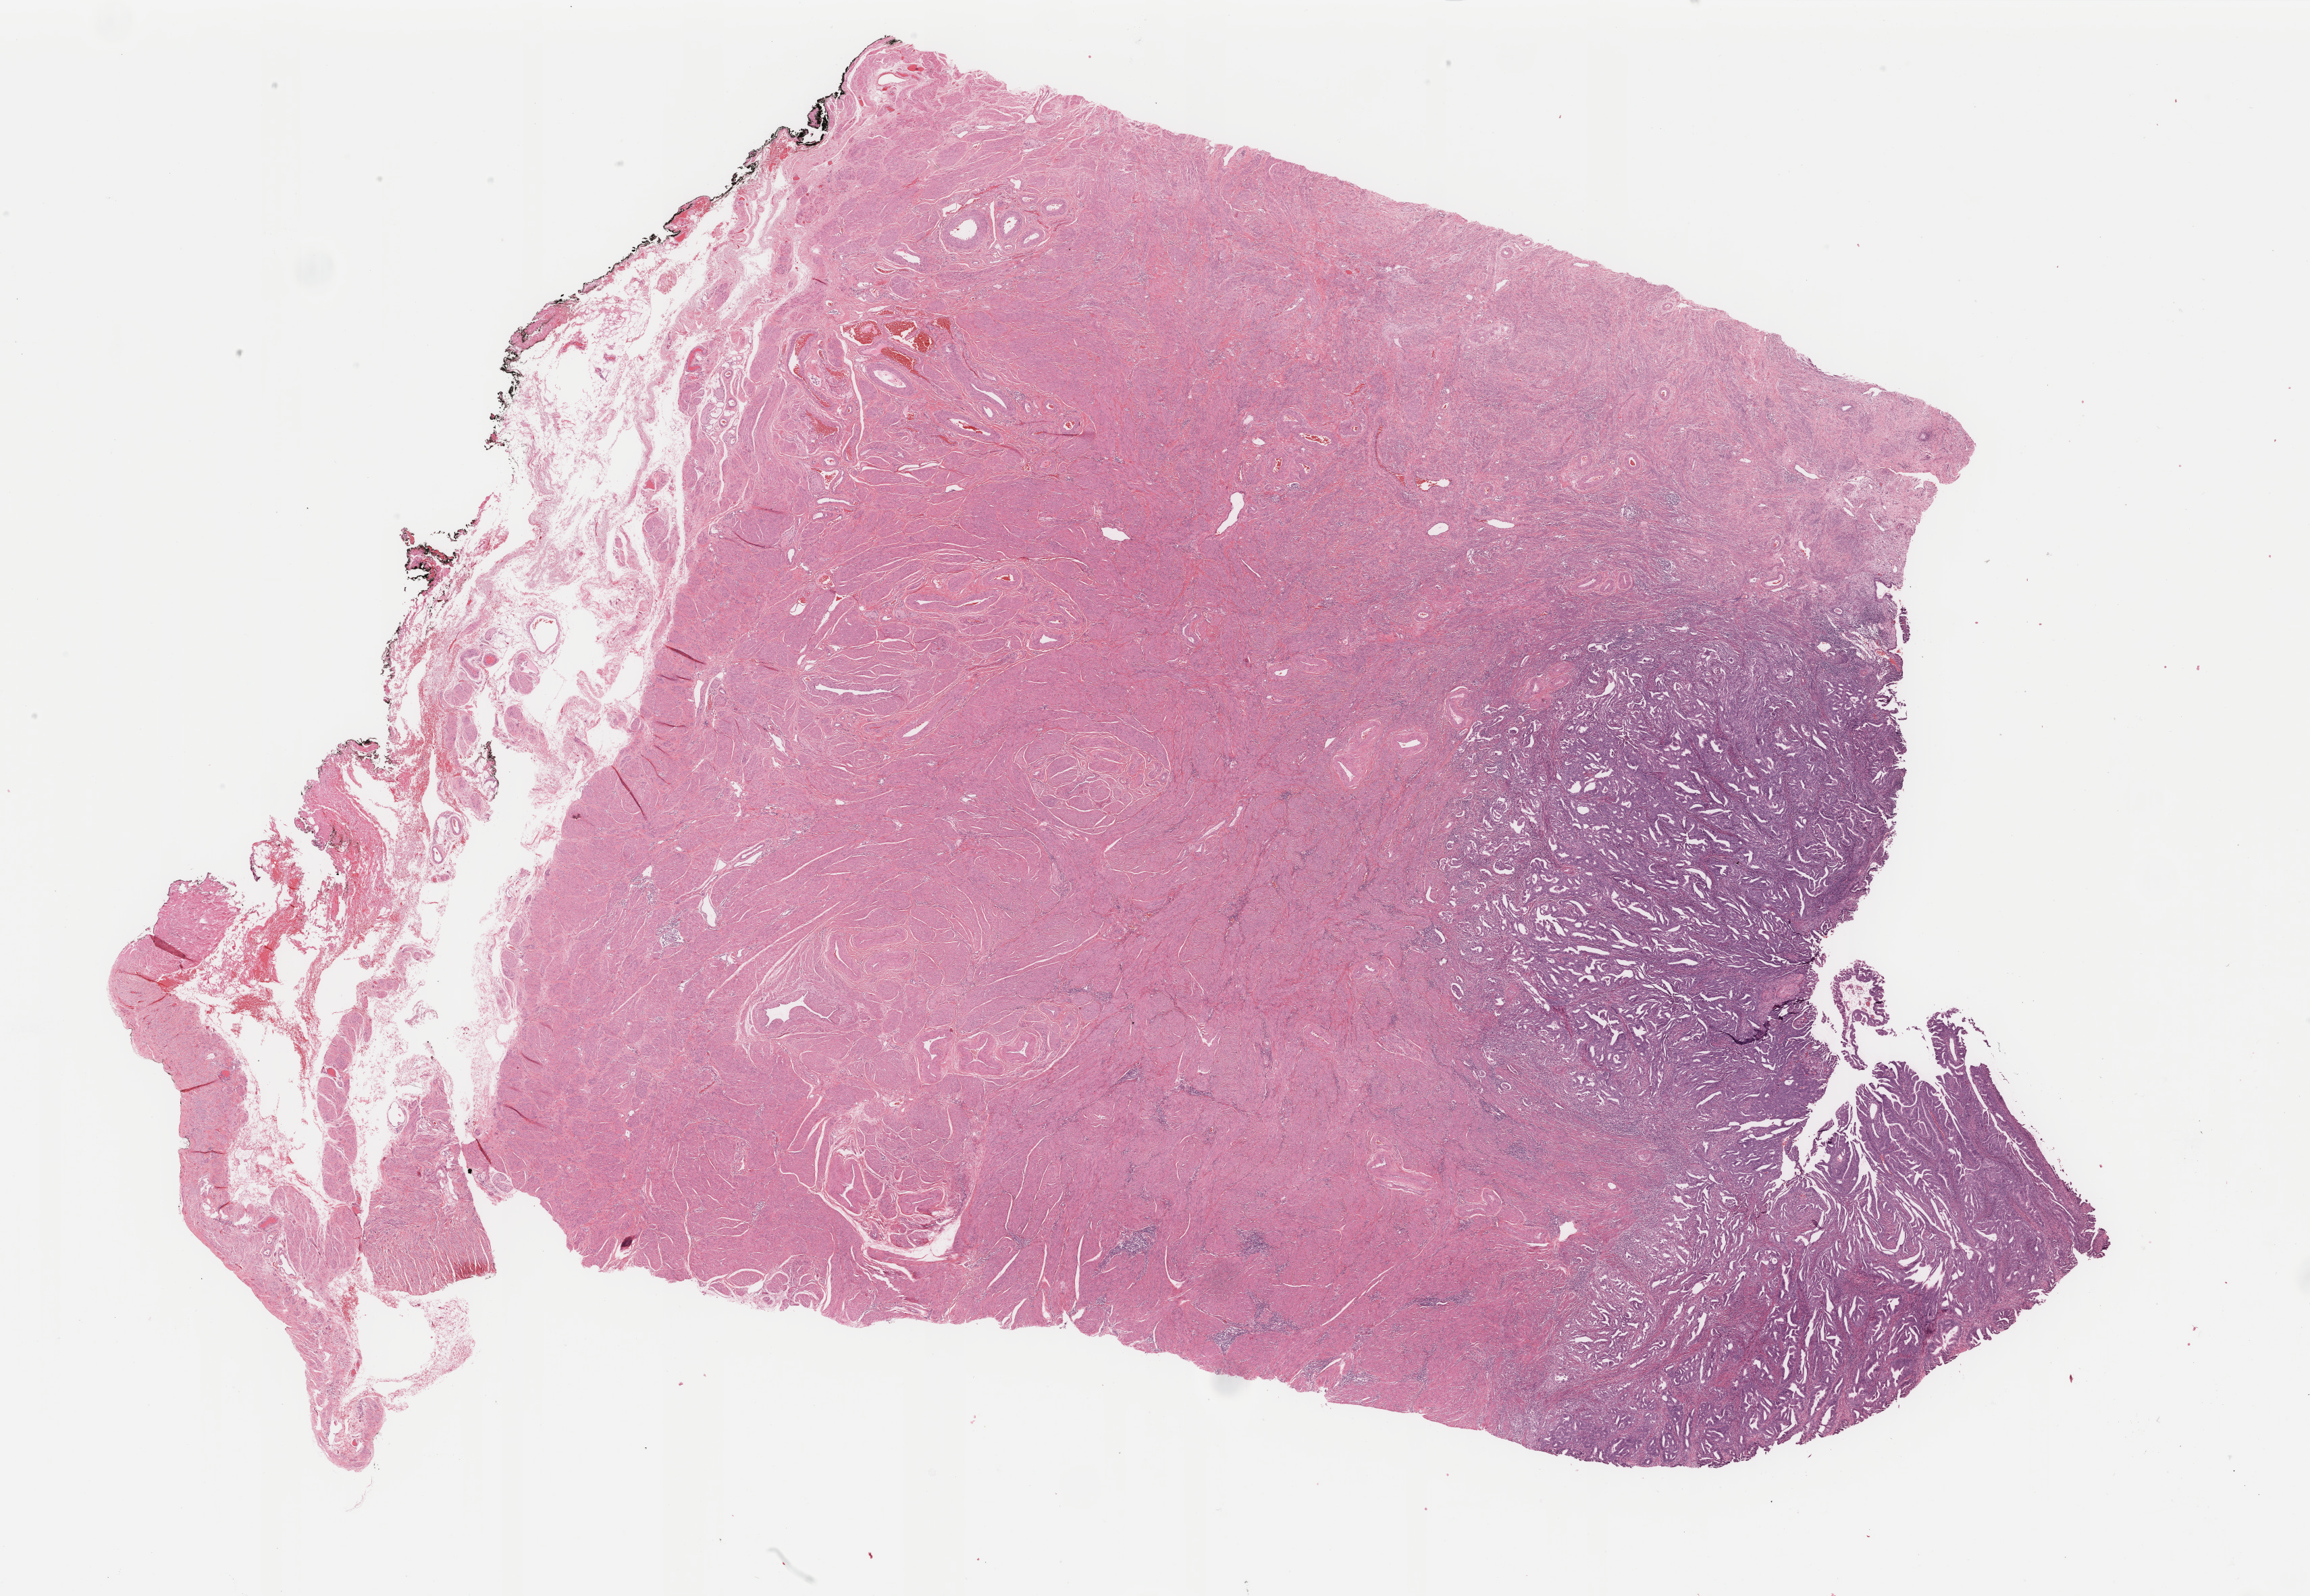
Digitized H&E-stained tissue section (whole slide), whole scanned area (about 27.2 x 18.8 mm, from a 40x scan) shown as a low-resolution overview. Formalin-fixed paraffin-embedded (FFPE) diagnostic section. Uterus, primary tumour sample. Patient: female, age at initial diagnosis 53 years. Histologic grade: G3 (poorly differentiated).
- diagnosis: Endometrioid adenocarcinoma, NOS (endometrium)
- lymph nodes positive (case pathology): 0 of 21 examined
- FIGO stage: IB